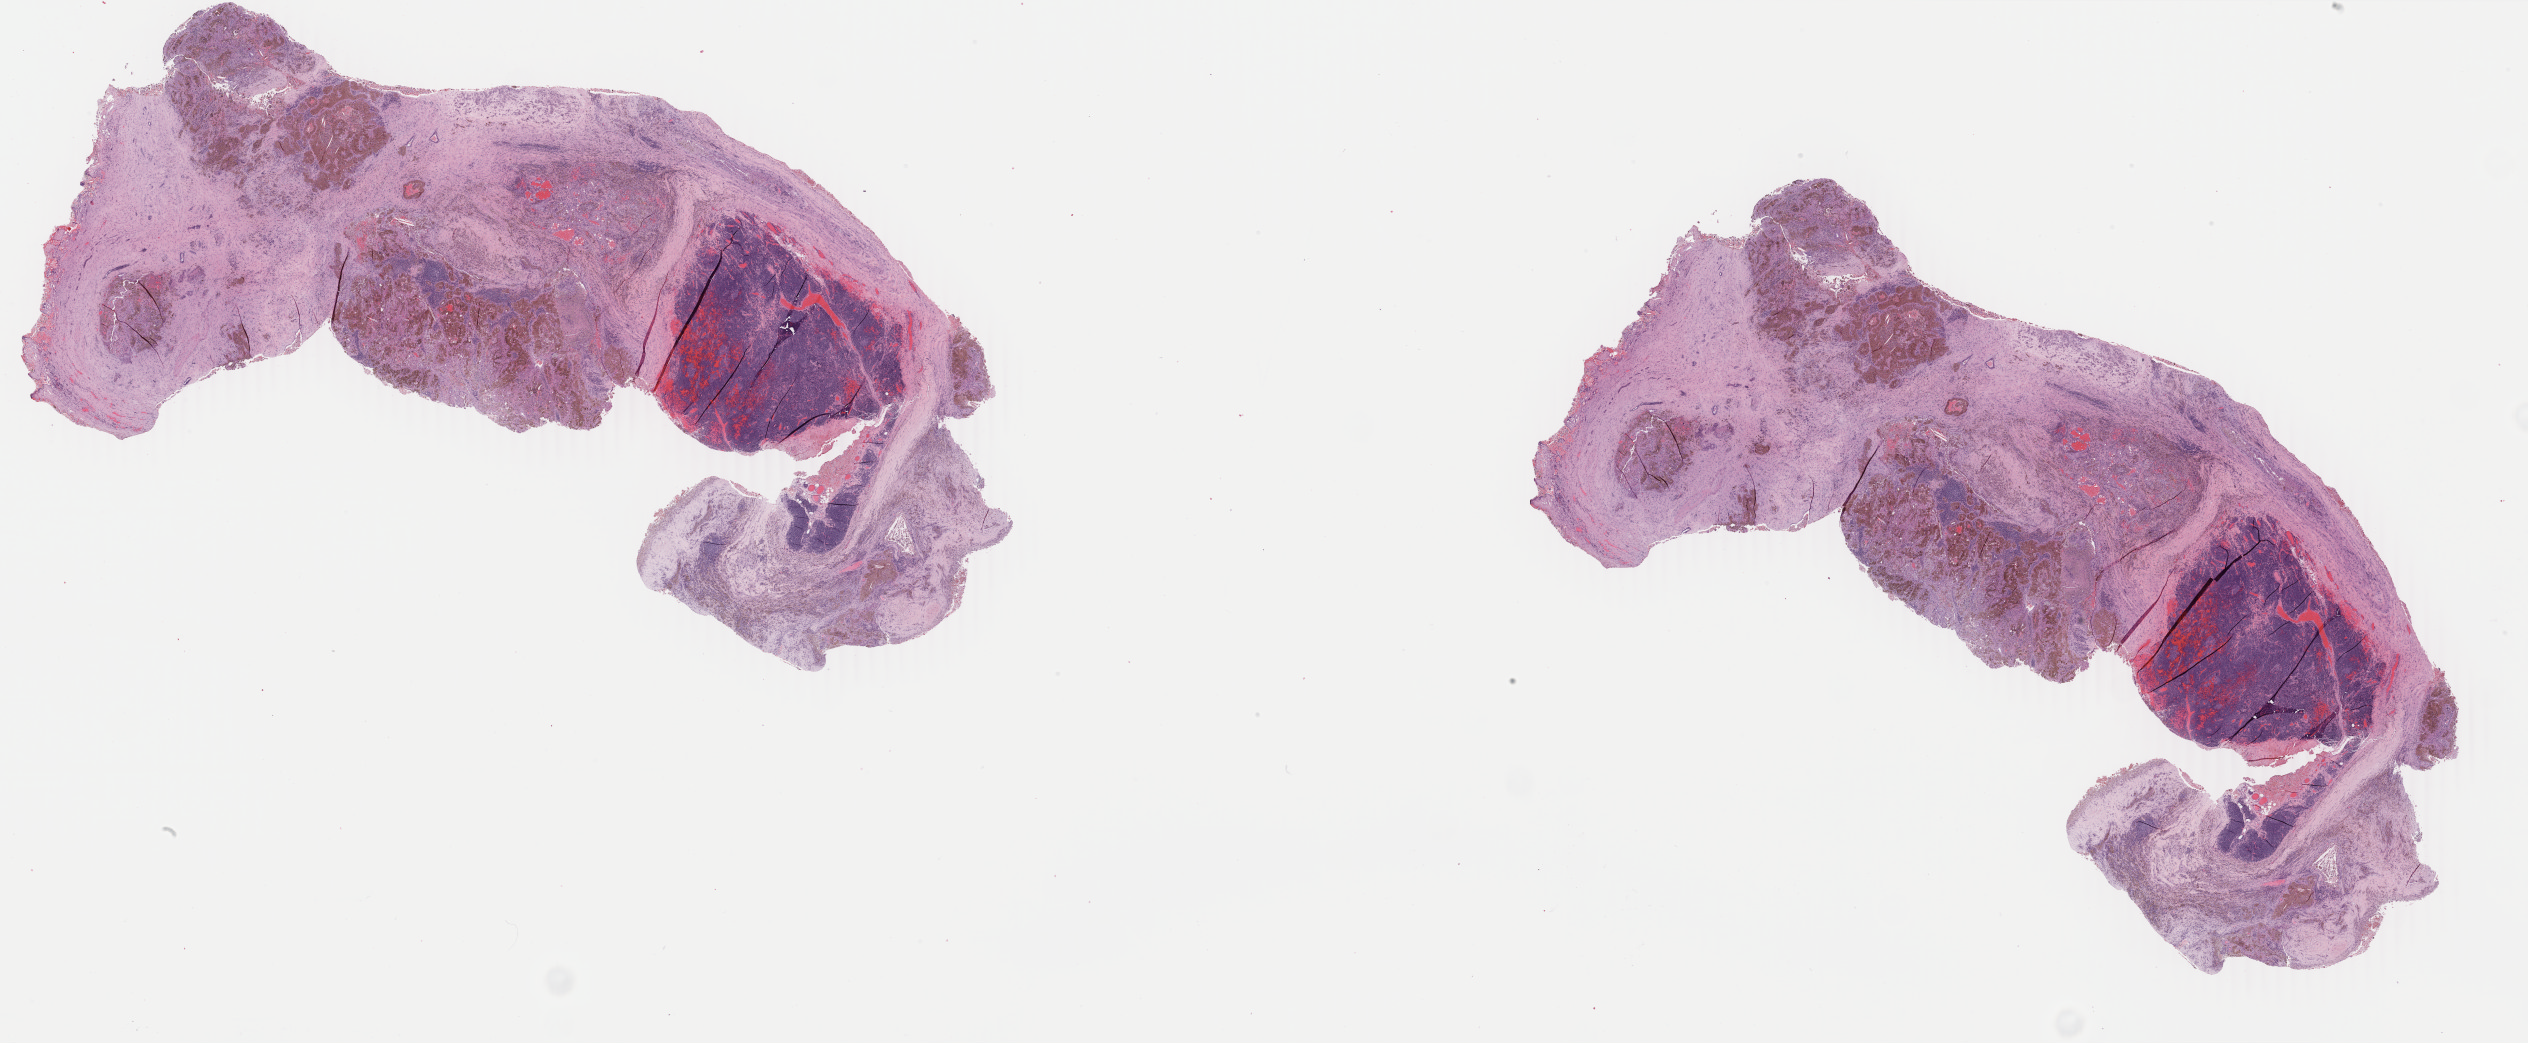
H&E whole-slide image, whole scanned area (about 40.2 x 16.6 mm) shown as a low-resolution overview, formalin-fixed paraffin-embedded (FFPE) diagnostic section, primary tumour sample from the kidney. Patient: male, age at initial diagnosis 61 years.
* pathologic diagnosis: Papillary adenocarcinoma, NOS
* AJCC pathologic stage: I (7th edition)